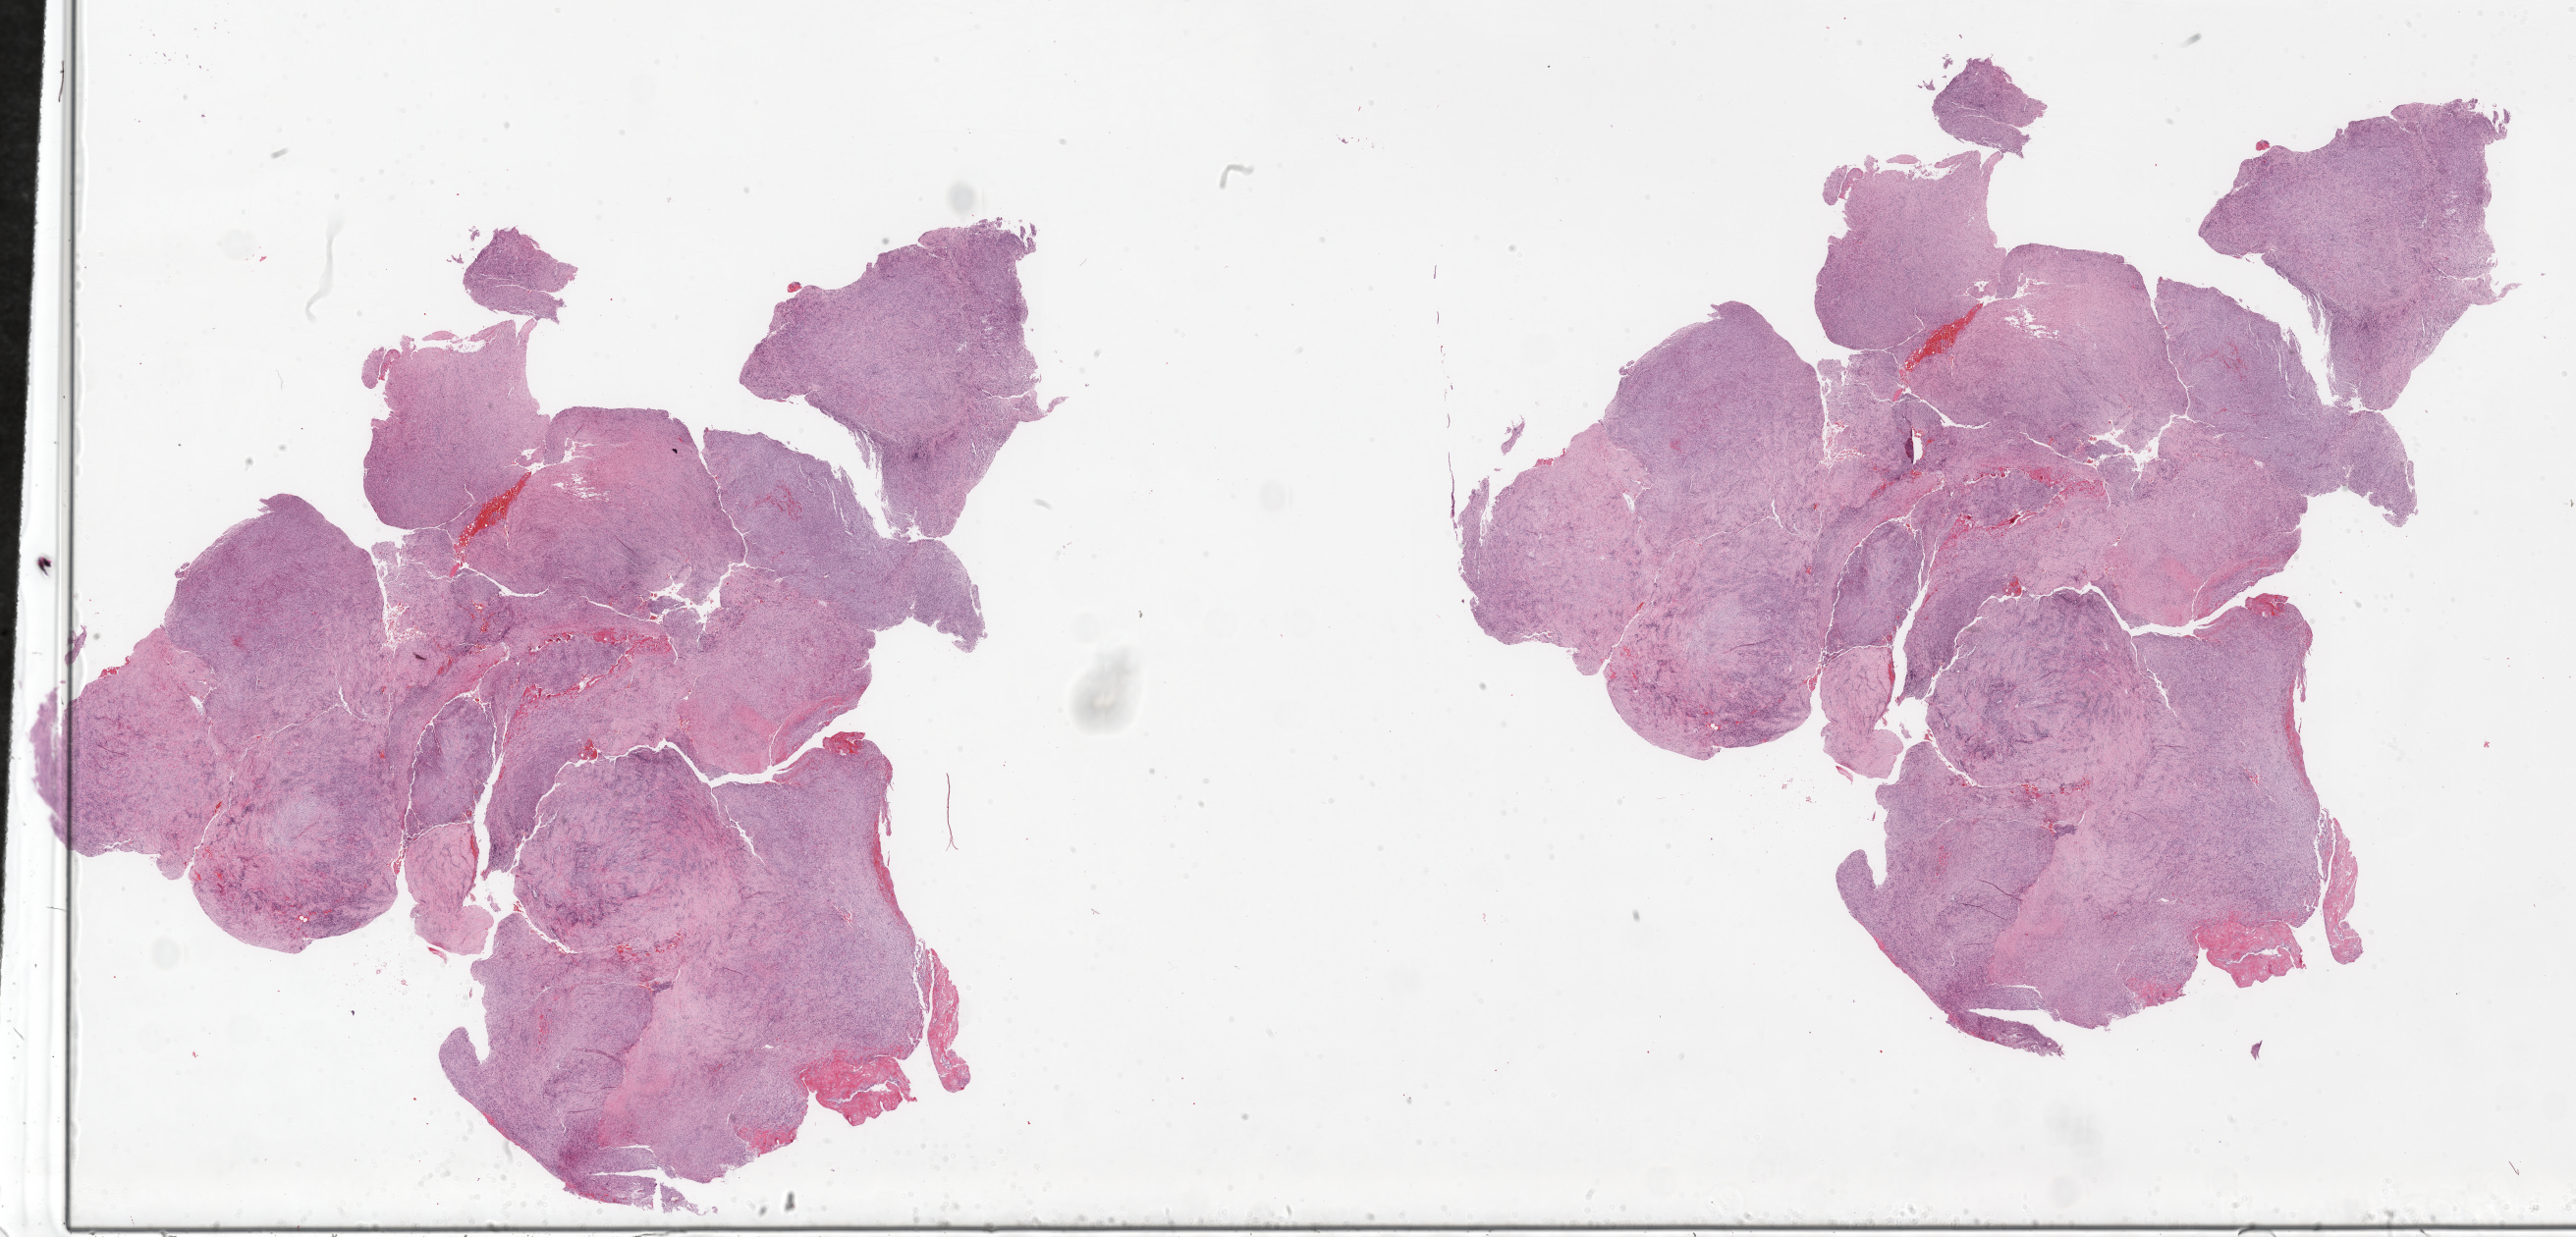
H&E whole-slide image, whole scanned area (about 42.1 x 20.2 mm, slide scanned at 20x) shown as a low-resolution overview; FFPE section; sample: primary tumour, mesothelium. Patient: male, age at initial diagnosis 58 years.
Laterality: right. Pathologic diagnosis: Mesothelioma, biphasic, malignant (pleura, NOS). AJCC pathologic stage: II.